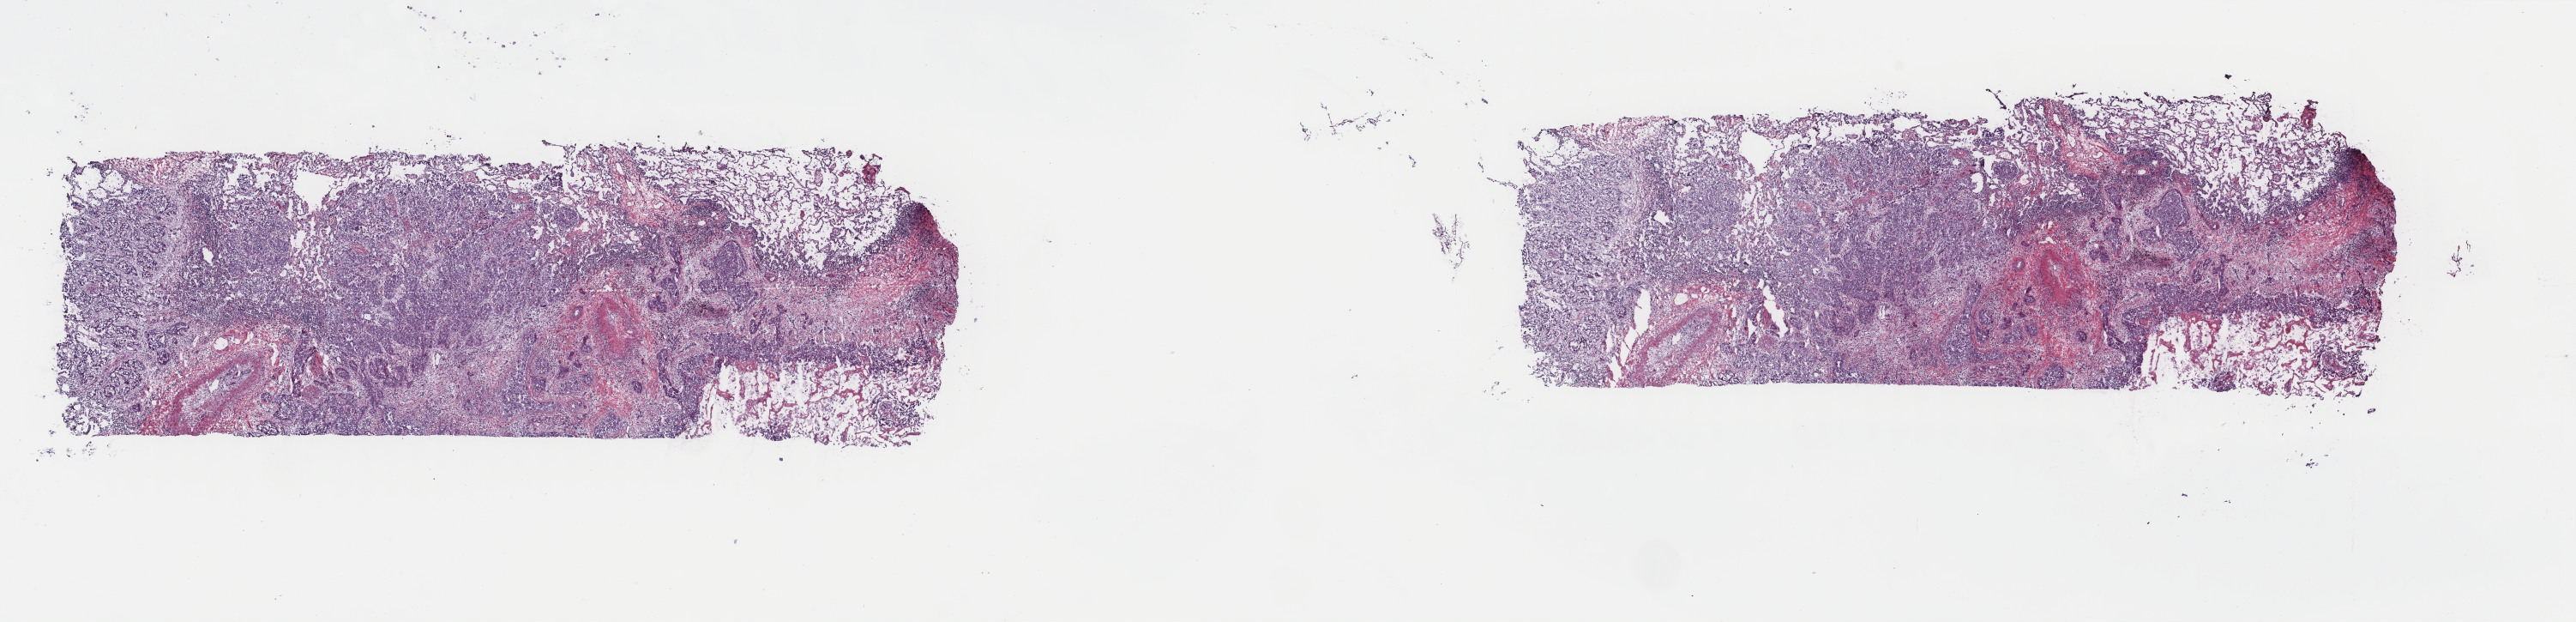
H&E-stained whole-slide image, shown as a low-resolution overview of the whole scanned area (about 23.8 x 5.8 mm, acquisition: 40x scan). Frozen section from the top of the tissue portion. Sample: primary tumour, lung. Female patient; age at initial diagnosis 54 years. Composition of this section per pathologist review: tumour cells 80%, tumour nuclei 75%, normal cells 20%, stromal cells 0%, necrosis 0%. Infiltration values recorded for this section: lymphocyte infiltration 0%, monocyte infiltration 0%, neutrophil infiltration 0%.
TNM: T2 N2 MX. AJCC pathologic stage: IIIA (6th edition). Diagnosis: Adenocarcinoma, NOS (upper lobe, lung).